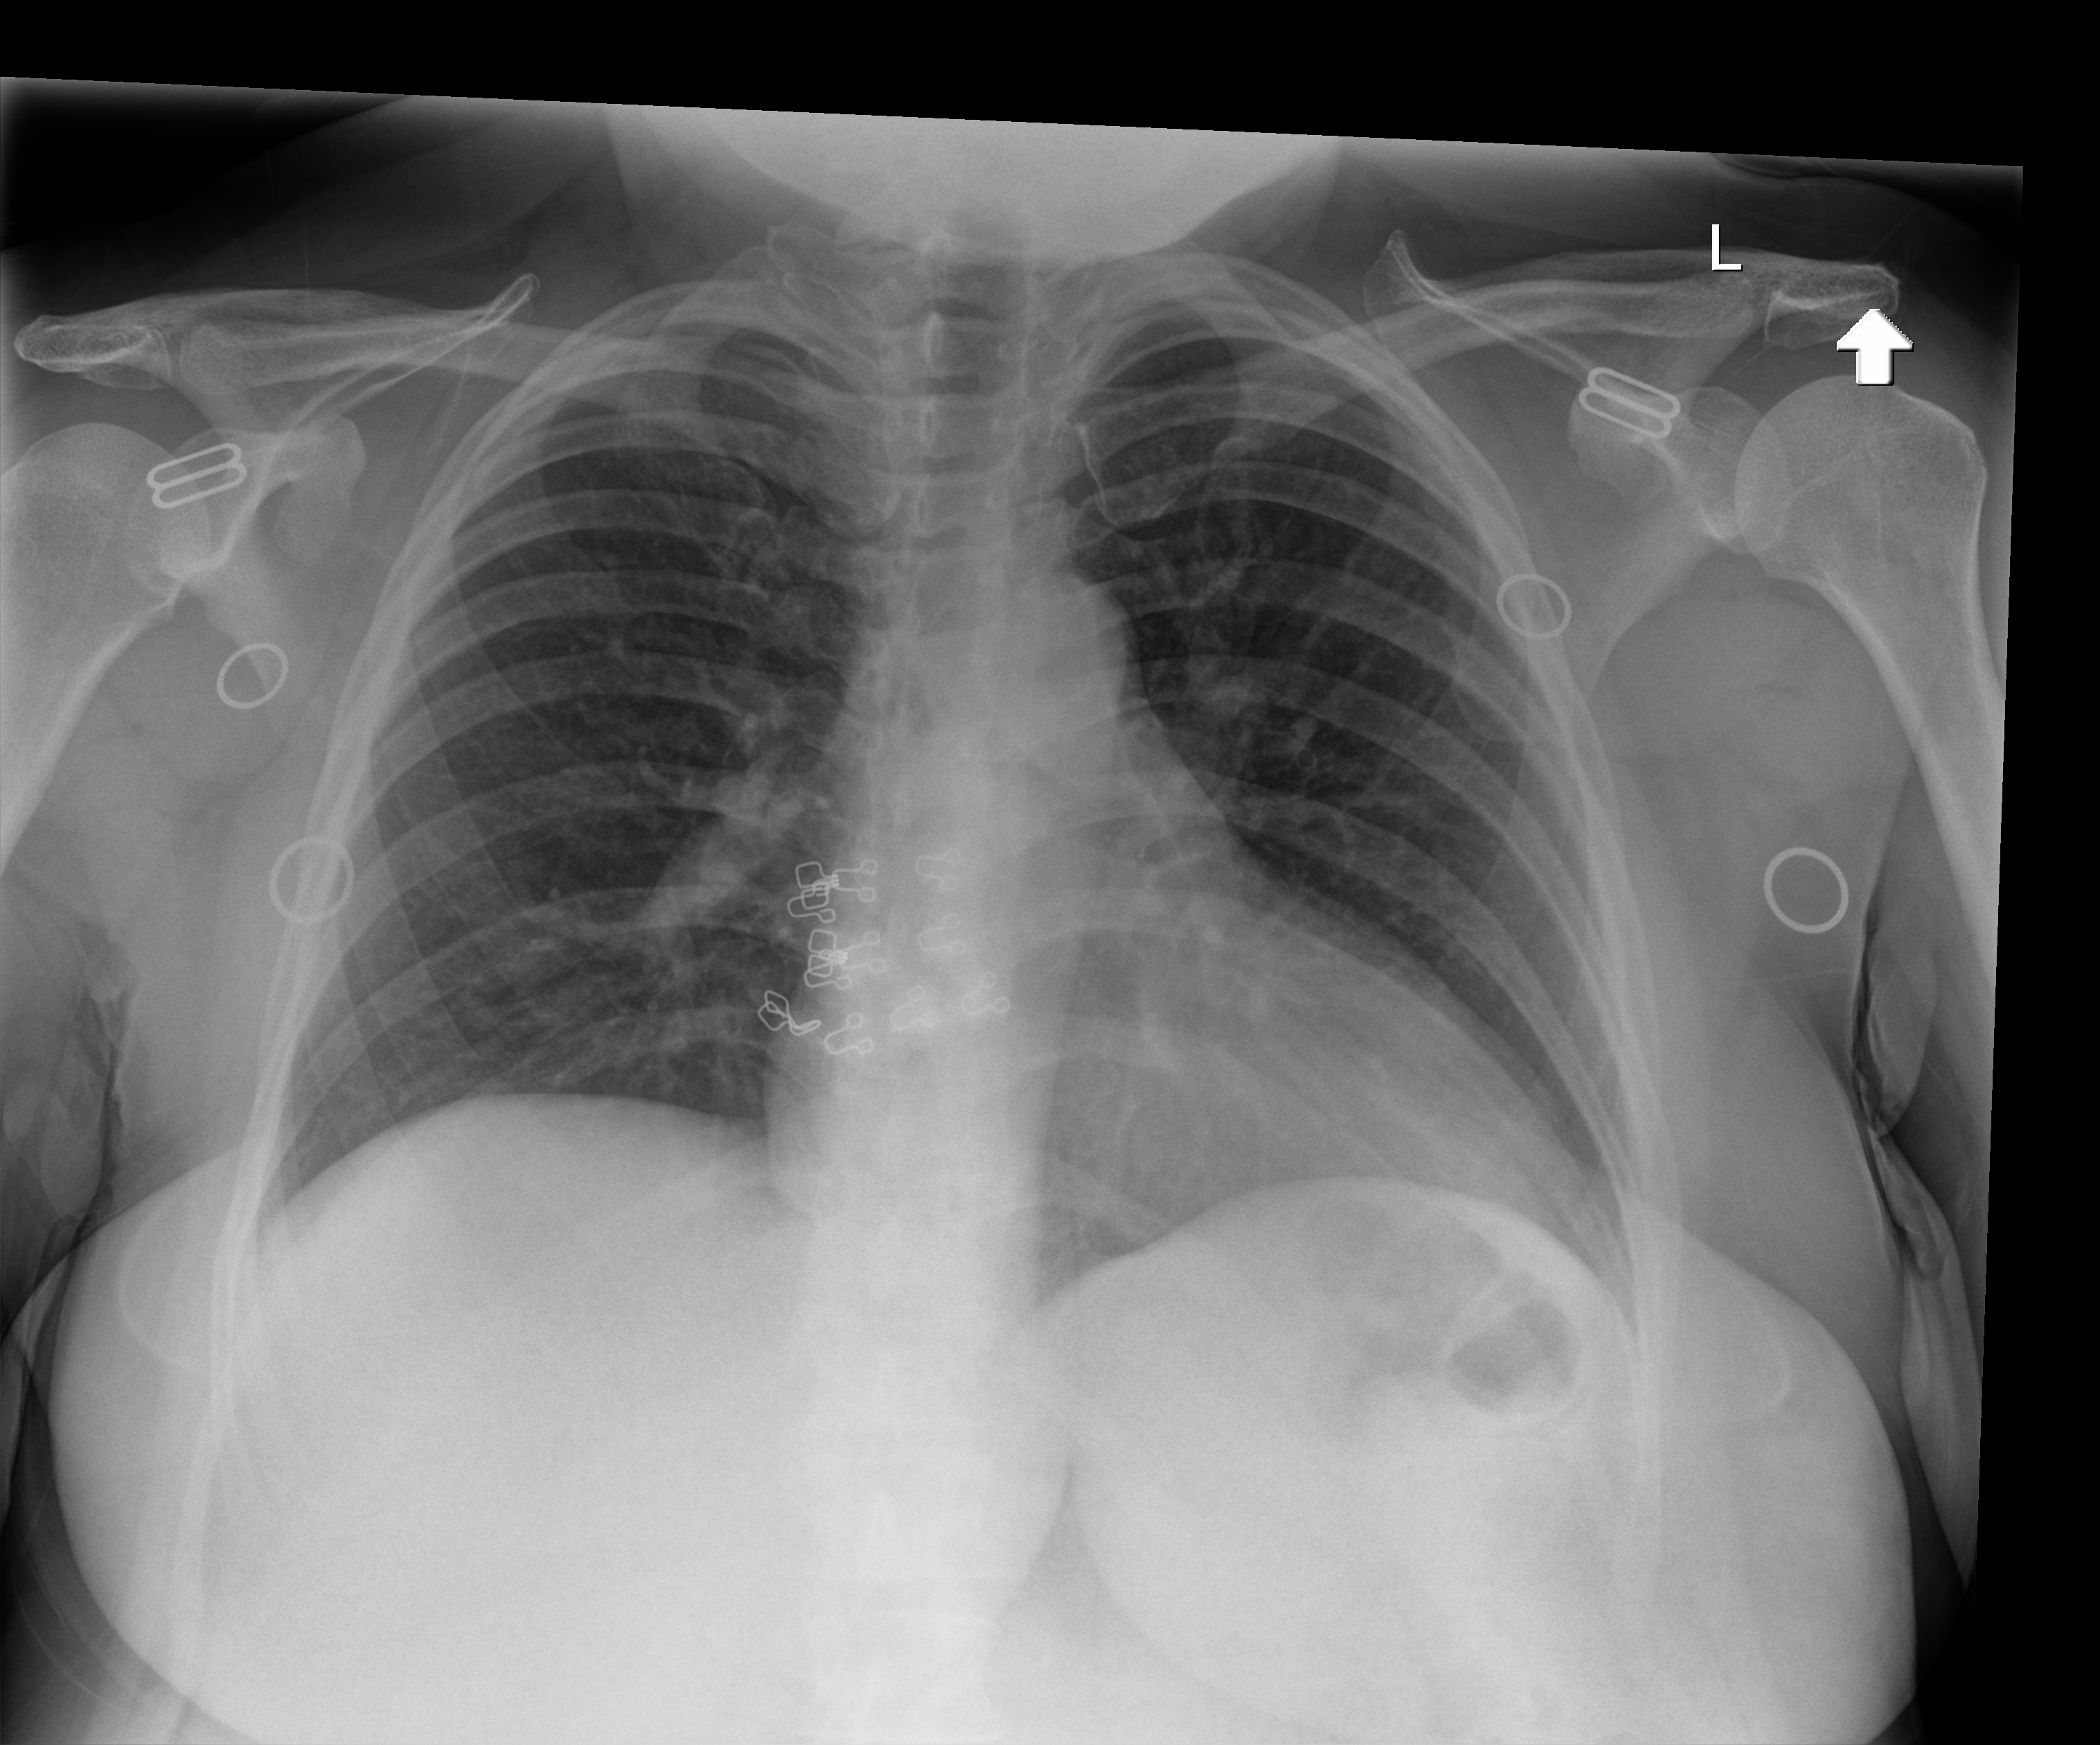
Chest X-ray (portable); anteroposterior (AP) projection. Female patient hospitalised with COVID-19, age 18–59 years.
Admission-level facts for this patient (not findings on this image; timing relative to this image not recorded):
- COPD (admission record): no